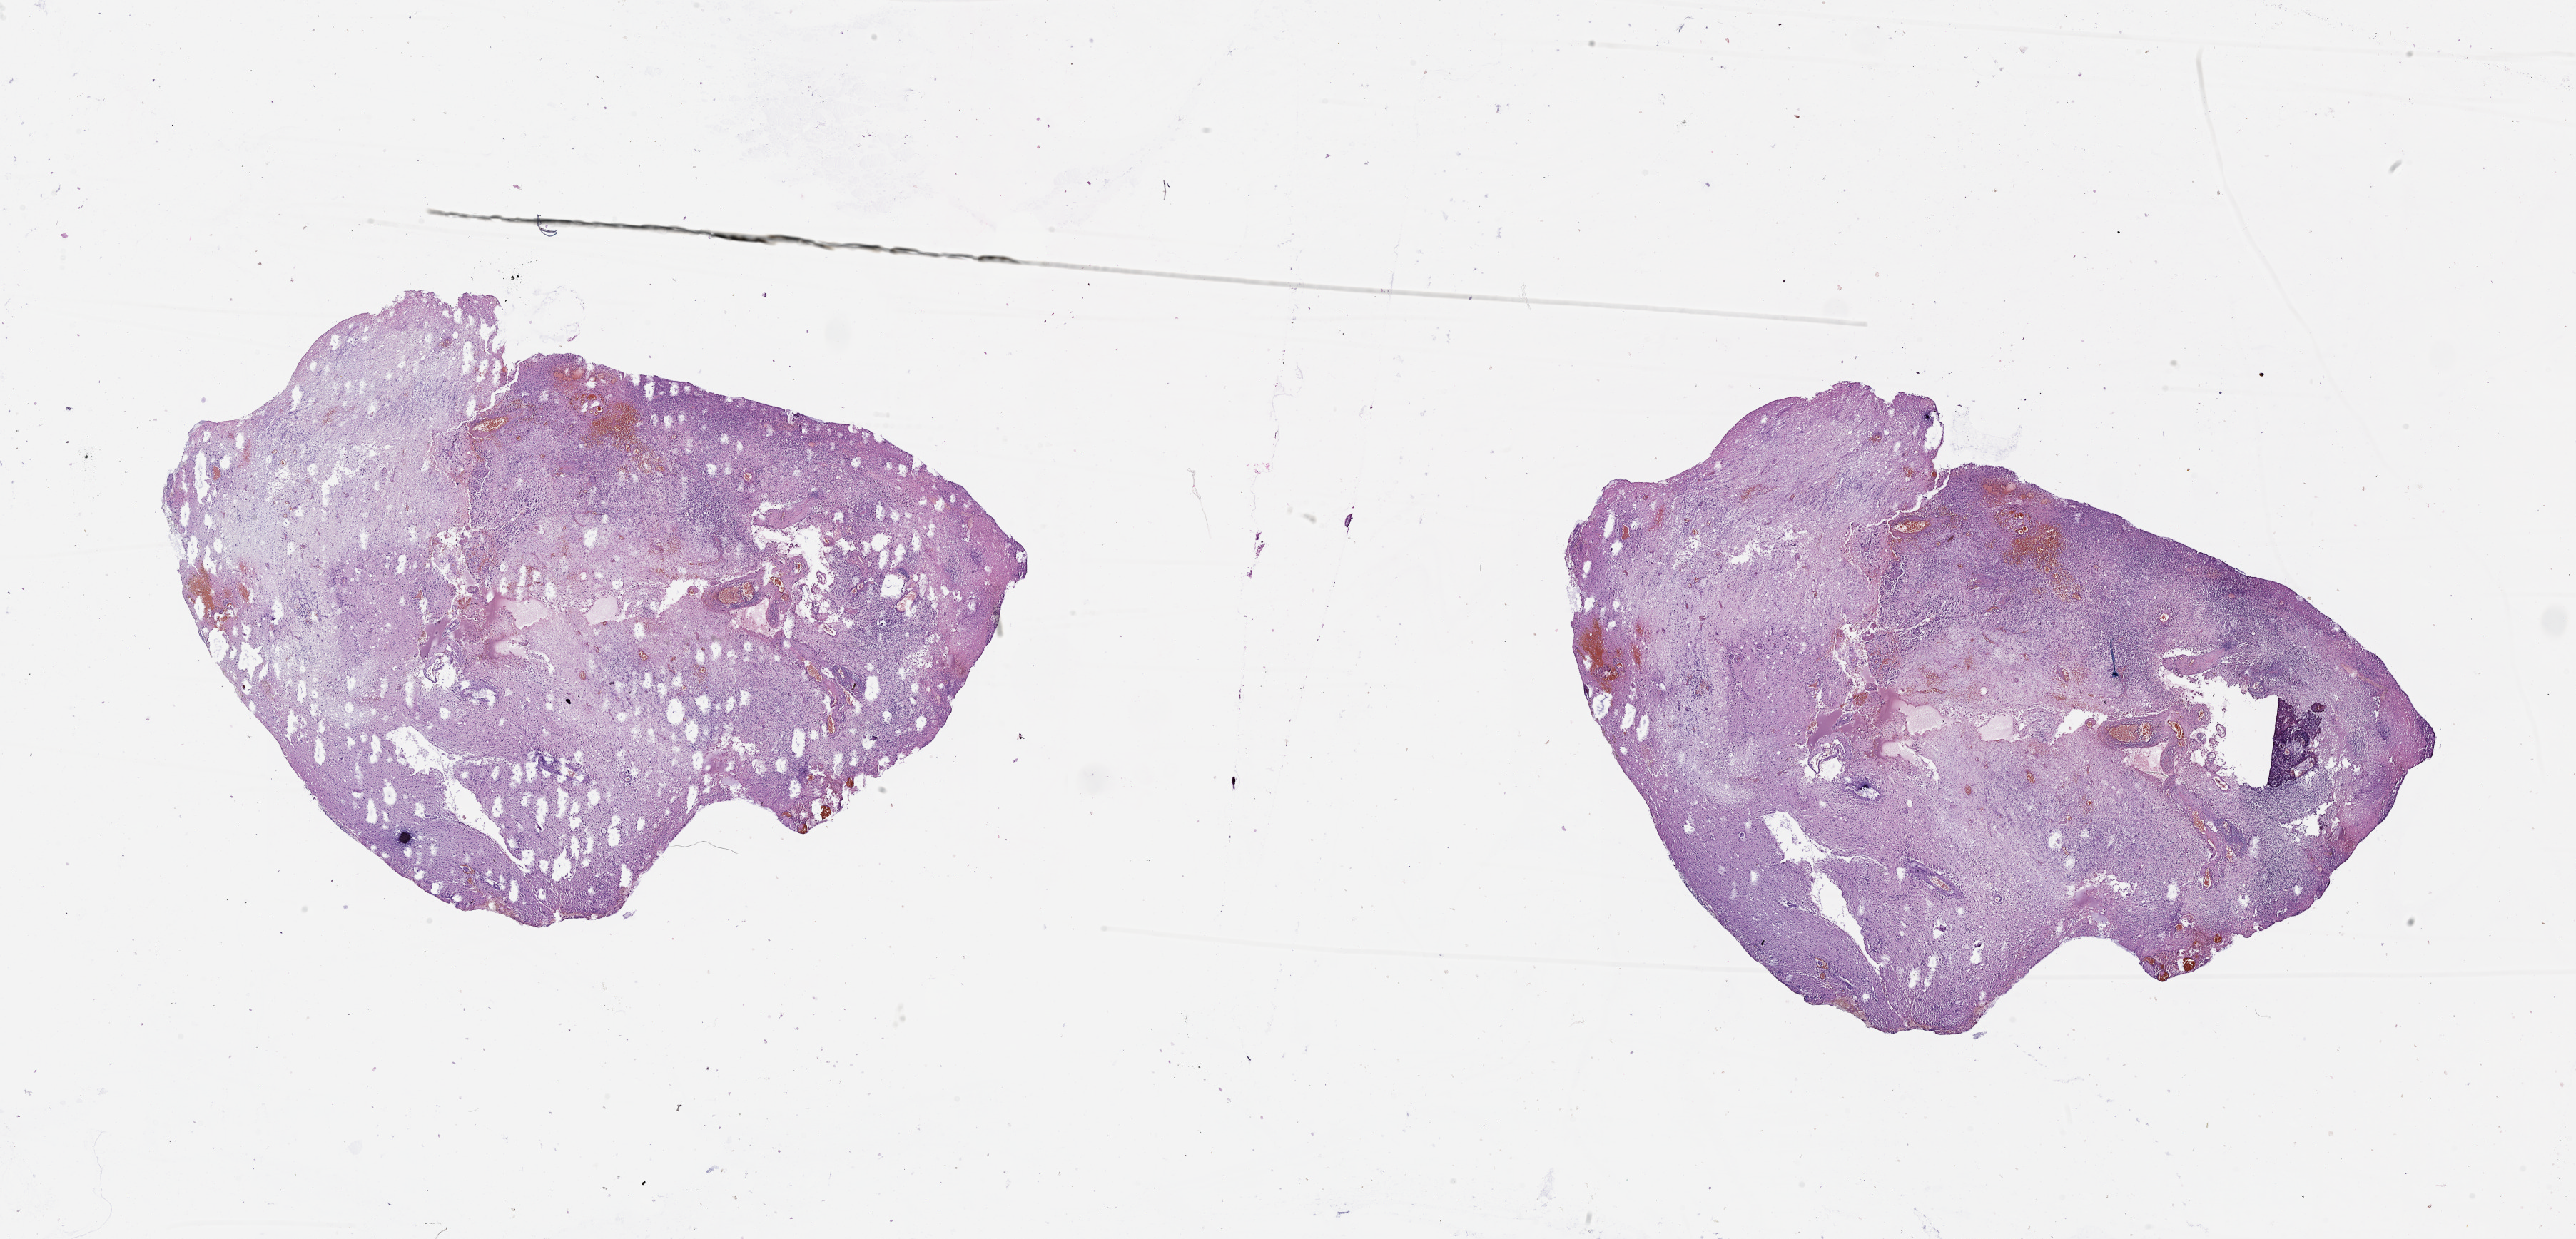
Whole-slide histology image, Hematoxylin and eosin (H&E) stained, shown as a low-resolution overview of the whole scanned area (about 29.1 x 14.0 mm, acquisition: 20x scan); brain, tumour tissue. Patient: male, age 63 years.
Primary tumour site (as recorded): frontal lobe. Histologic diagnosis: Glioblastoma.